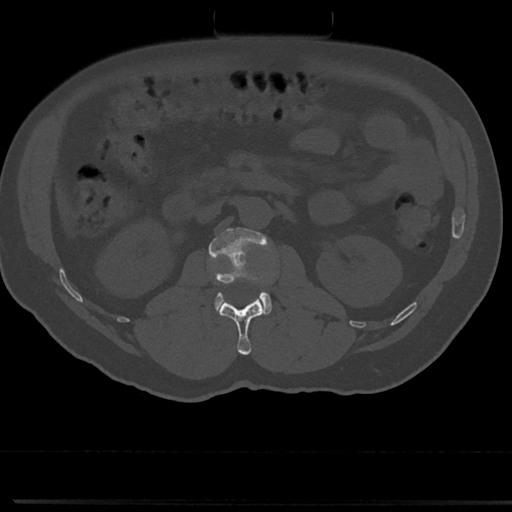
CT including the spine, one axial slice. Slice 47 of 817 in the series (ordered by position). 120 kVp. Bone window (W 1800 / L 400 HU). 512 × 512 image matrix. Male patient, age 61 years. From the clinical record (not read from this slice): primary cancer: prostate.
Annotated regions visible in this slice (semi-automatic segmentation, software-assisted and operator-edited):
- L1 vertebra: bounding box <219,297,264,355> (left, top, right, bottom; pixels)
- L2 vertebra: <209,227,272,315>